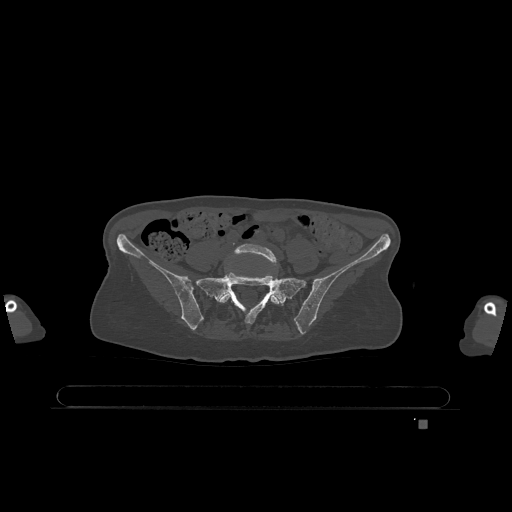
CT including the spine, one axial slice; slice 208 of 1317 in the series (ordered by position); bone window (W 1800 / L 400 HU); 512 × 512 image matrix, field of view 500 × 500 mm. Female patient, age 74 years. Case-level facts recorded for this patient, not image findings: primary cancer: lung; vertebrae with lytic lesions (as recorded): T1, T4, T5, T6, L4, L5.
Outlined on this slice (semi-automatic segmentation, software-assisted and operator-edited):
- L5 vertebra: bounding box (x1, y1, x2, y2) in pixels: (219, 243, 283, 306)